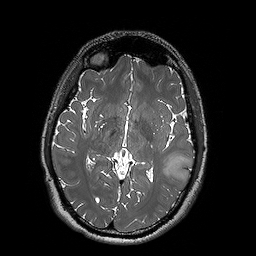
Brain MRI from a brain-tumour surgery series, one axial slice; 256 × 256 image matrix, field of view 250 × 250 mm. Case-level facts recorded for this patient, not image findings: histopathology: Oligodendroglioma; WHO grade: 2; IDH mutation: yes; tumour location: Left Posterior Temporal.
Structures marked on this image (outlined manually by an expert reader):
- tumour: bounding box (x1, y1, x2, y2) in pixels: (159, 155, 193, 182)